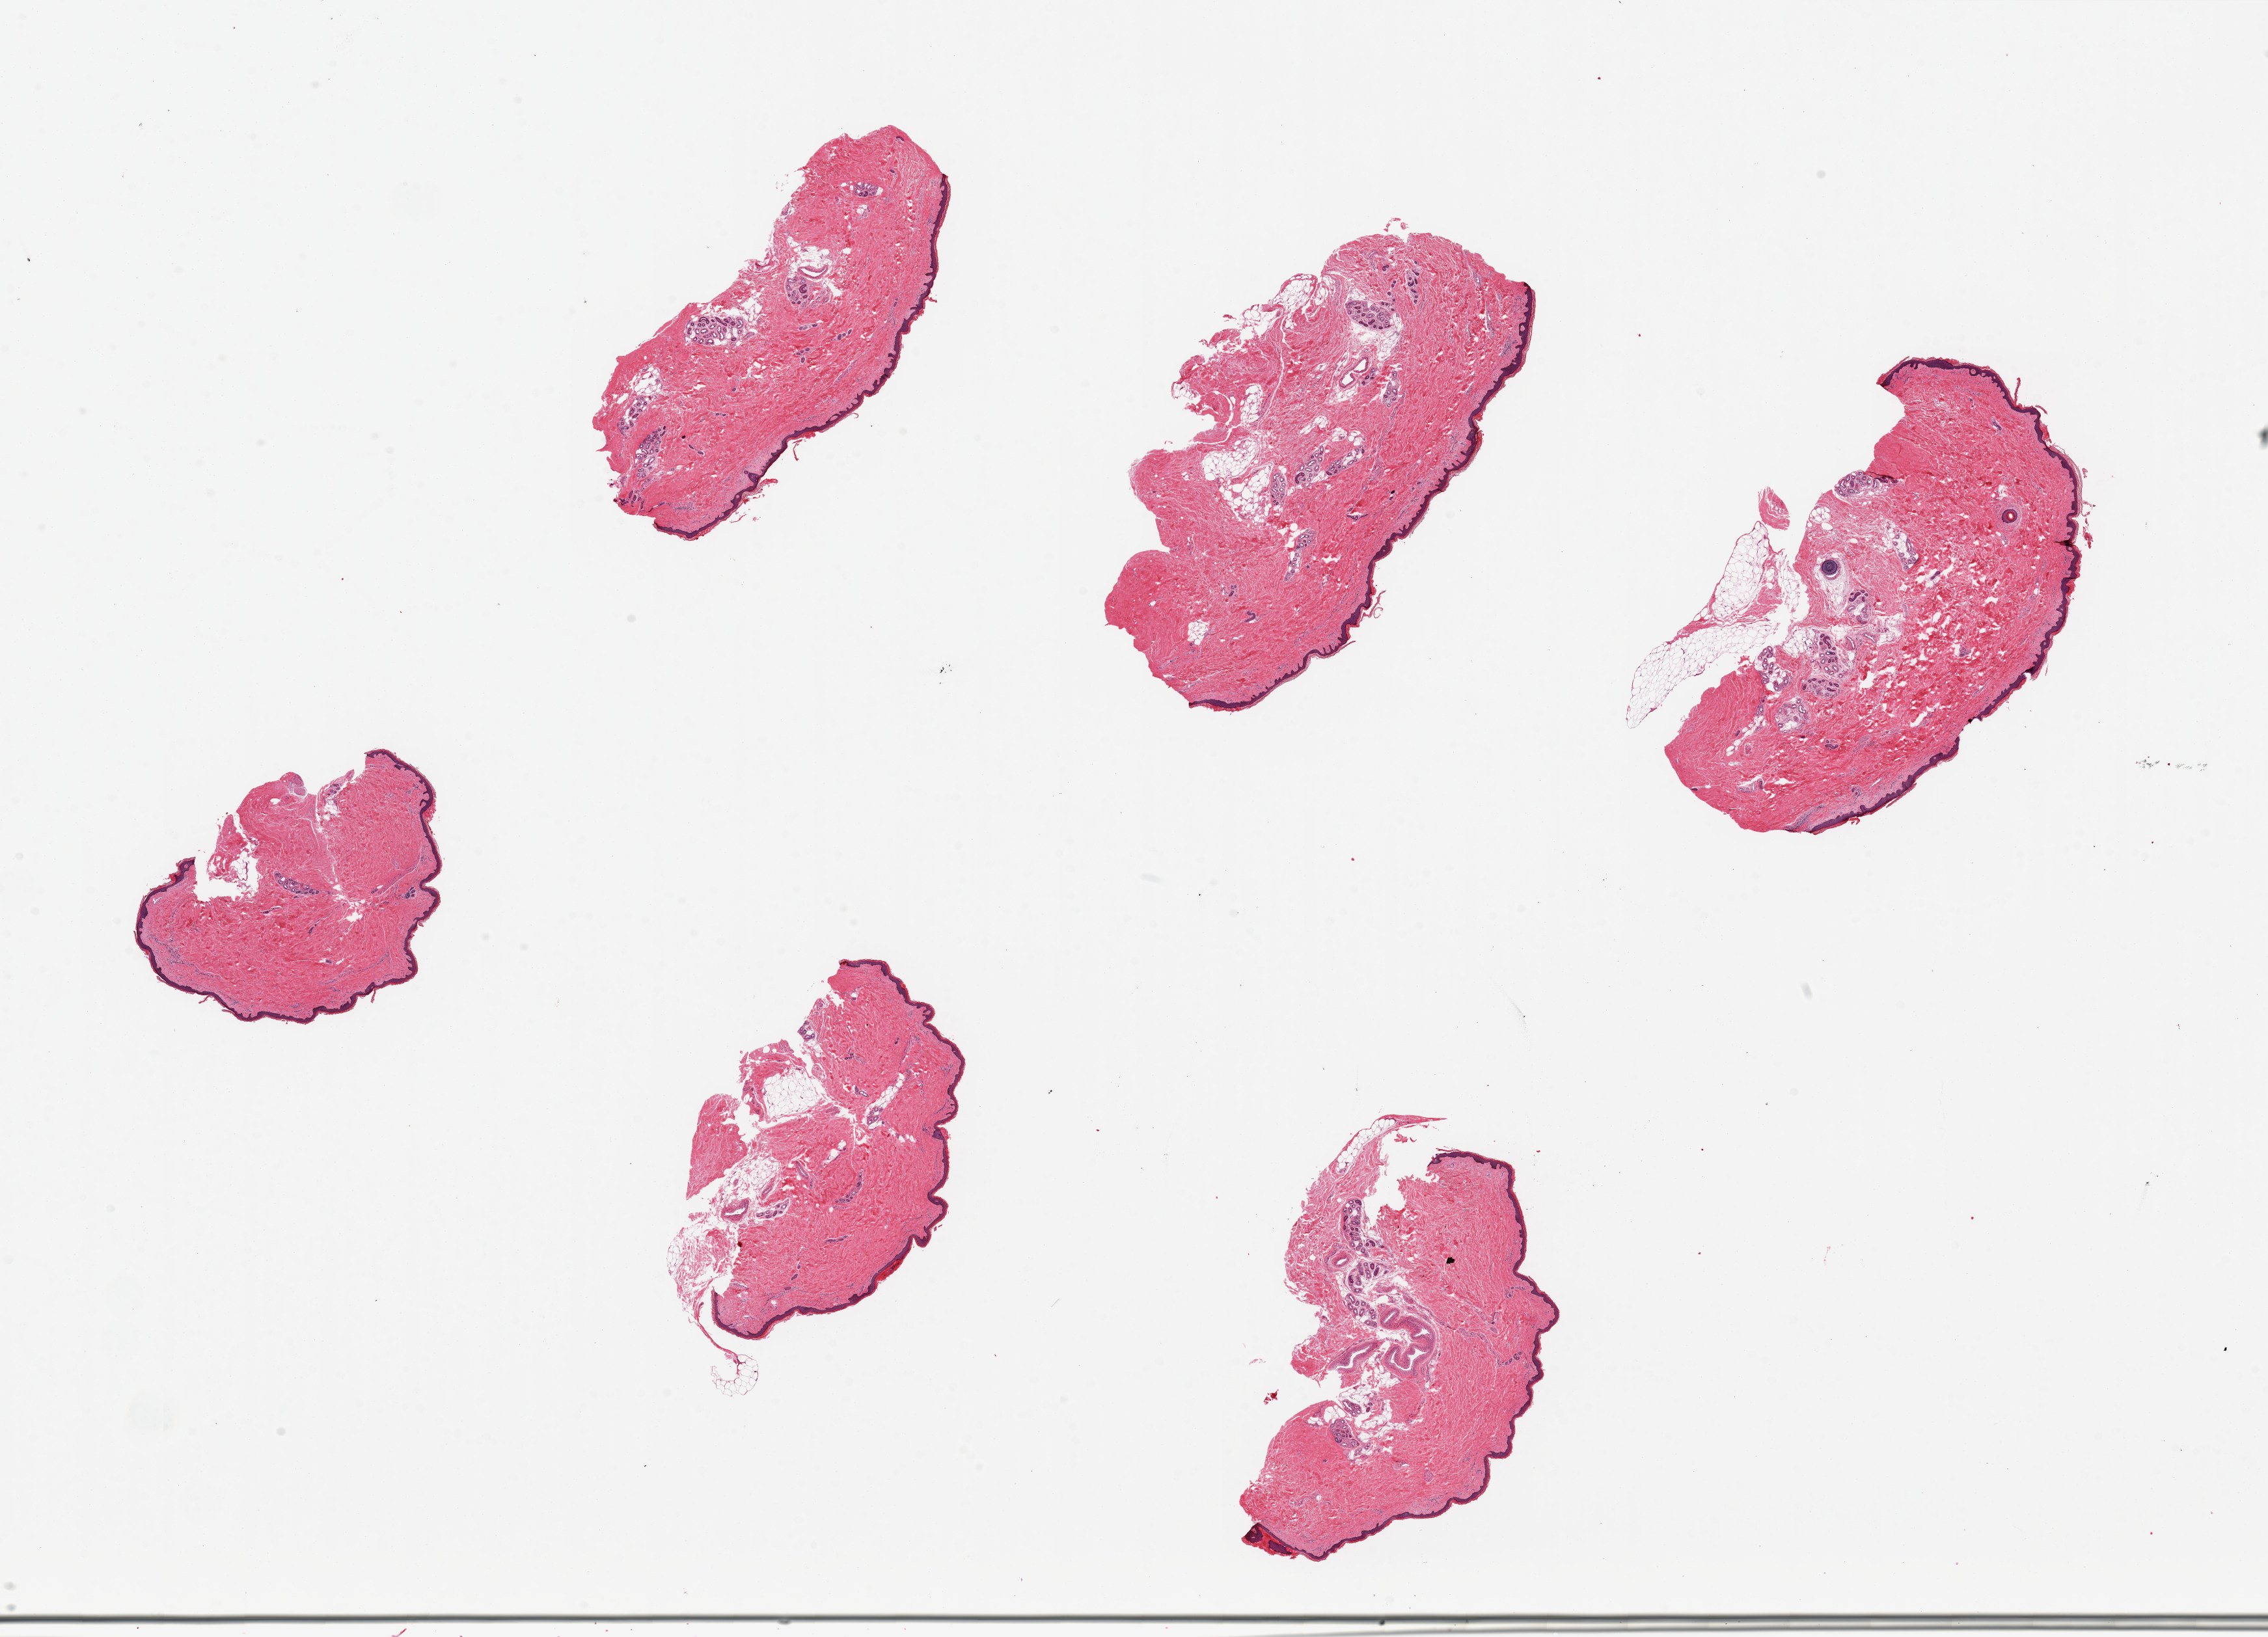
Hematoxylin and eosin (H&E) whole-slide image, brightfield — a low-resolution overview of the entire scanned area, about 27.6 x 19.9 mm (slide scanned at 20x), PAXgene-fixed paraffin-embedded (PFPE) section, sampled site (target tissue): skin of lower leg, tissue donor sample. Donor sex: male.
Pathologist's review note for this sample: 6 pieces, ~6x3mm squamous mucosa is ~2-3% of thickness or ~50 microns thick.